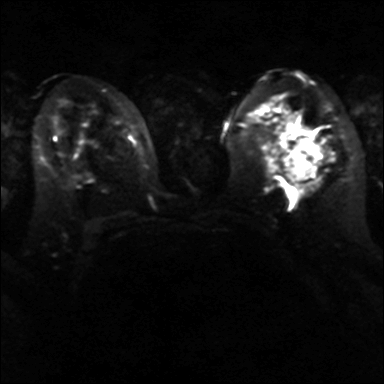
Breast MRI, one axial slice. Position 22 of 40 along the scan axis. Diffusion-weighted series; image 2 of 4 stored at this slice position (different b-values; order by instance number). 3 T. 384 × 384 image matrix, field of view 320 × 320 mm. Female patient.
Annotated regions visible in this slice (outlined manually by an expert reader):
- tumour on diffusion-weighted imaging: box from (x=285, y=141) to (x=319, y=180) px